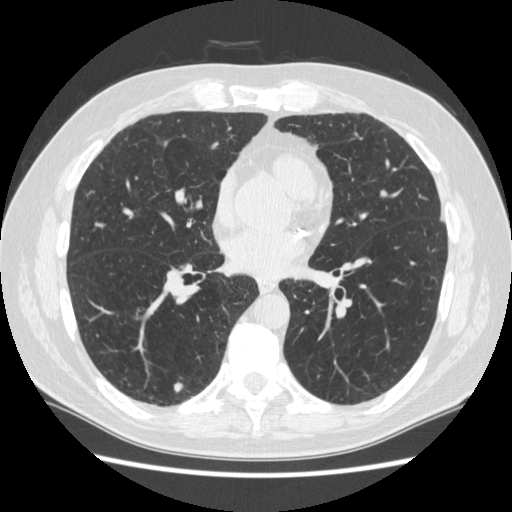
Low-dose screening chest CT, one axial slice. Slice 121 of 267 in the series (ordered by position). Reconstruction kernel STANDARD. Lung window (W 1500 / L -600 HU). 1.25 mm slice thickness. 512 × 512 image matrix, field of view 360 × 360 mm.
Annotated regions visible in this slice (manually delineated by an expert):
- lesion 3 (nodule, lower lobe of right lung): bounding box <174,383,183,393> (left, top, right, bottom; pixels)